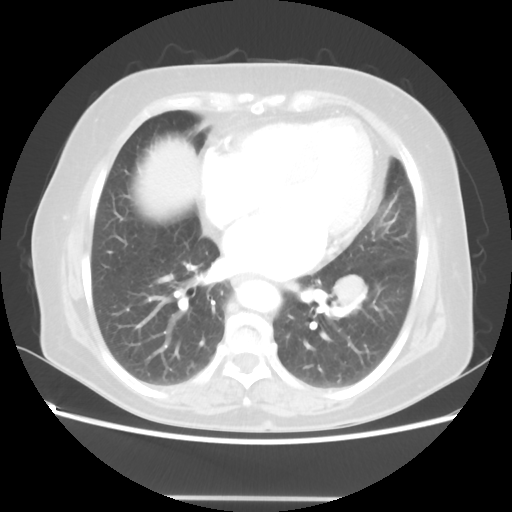
Chest CT, one axial slice; slice 23 of 56 in the series (ordered by position); reconstruction kernel STANDARD; lung window (W 1500 / L -600 HU); 512 × 512 image matrix. Patient: female, 73 years. From the clinical record (not read from this slice): clinical TNM (as recorded): T1c N0 M0.
Outlined on this slice (bounding box drawn by a radiologist):
- lung tumour (recorded histology: adenocarcinoma): bounding box [x1, y1, x2, y2] px = [333, 268, 366, 317]